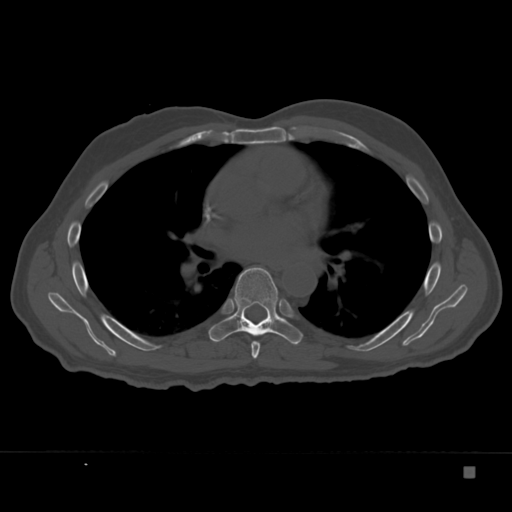
CT including the spine, one axial slice. Position 227 of 332 along the scan axis. 120 kVp. Bone window (W 1800 / L 400 HU). 512 × 512 image matrix, field of view 389 × 389 mm. Patient: male, 72 years. From the clinical record (not read from this slice): primary cancer: skeletal.
Annotated regions visible in this slice (semi-automatically segmented with operator editing):
- T6 vertebra: bounding box [x1, y1, x2, y2] px = [251, 341, 260, 359]
- T7 vertebra: [209, 267, 303, 345]